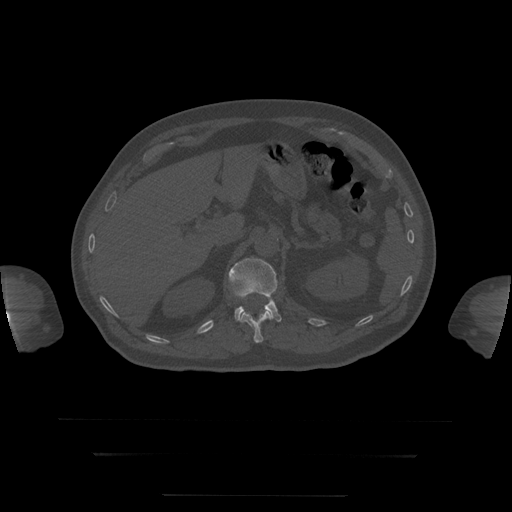
CT including the spine, one axial slice; position 61 of 397 along the scan axis; 120 kVp; bone window (W 1800 / L 400 HU); 1.25 mm slice thickness; 512 × 512 image matrix. Patient age 73 years. From the clinical record (not read from this slice): primary cancer: prostate.
Structures marked on this image (semi-automatically segmented with operator editing):
- L1 vertebra: bounding box (x1, y1, x2, y2) in pixels: (229, 258, 282, 322)
- T12 vertebra: (240, 311, 272, 343)
- T8 vertebra: (265, 305, 269, 311)